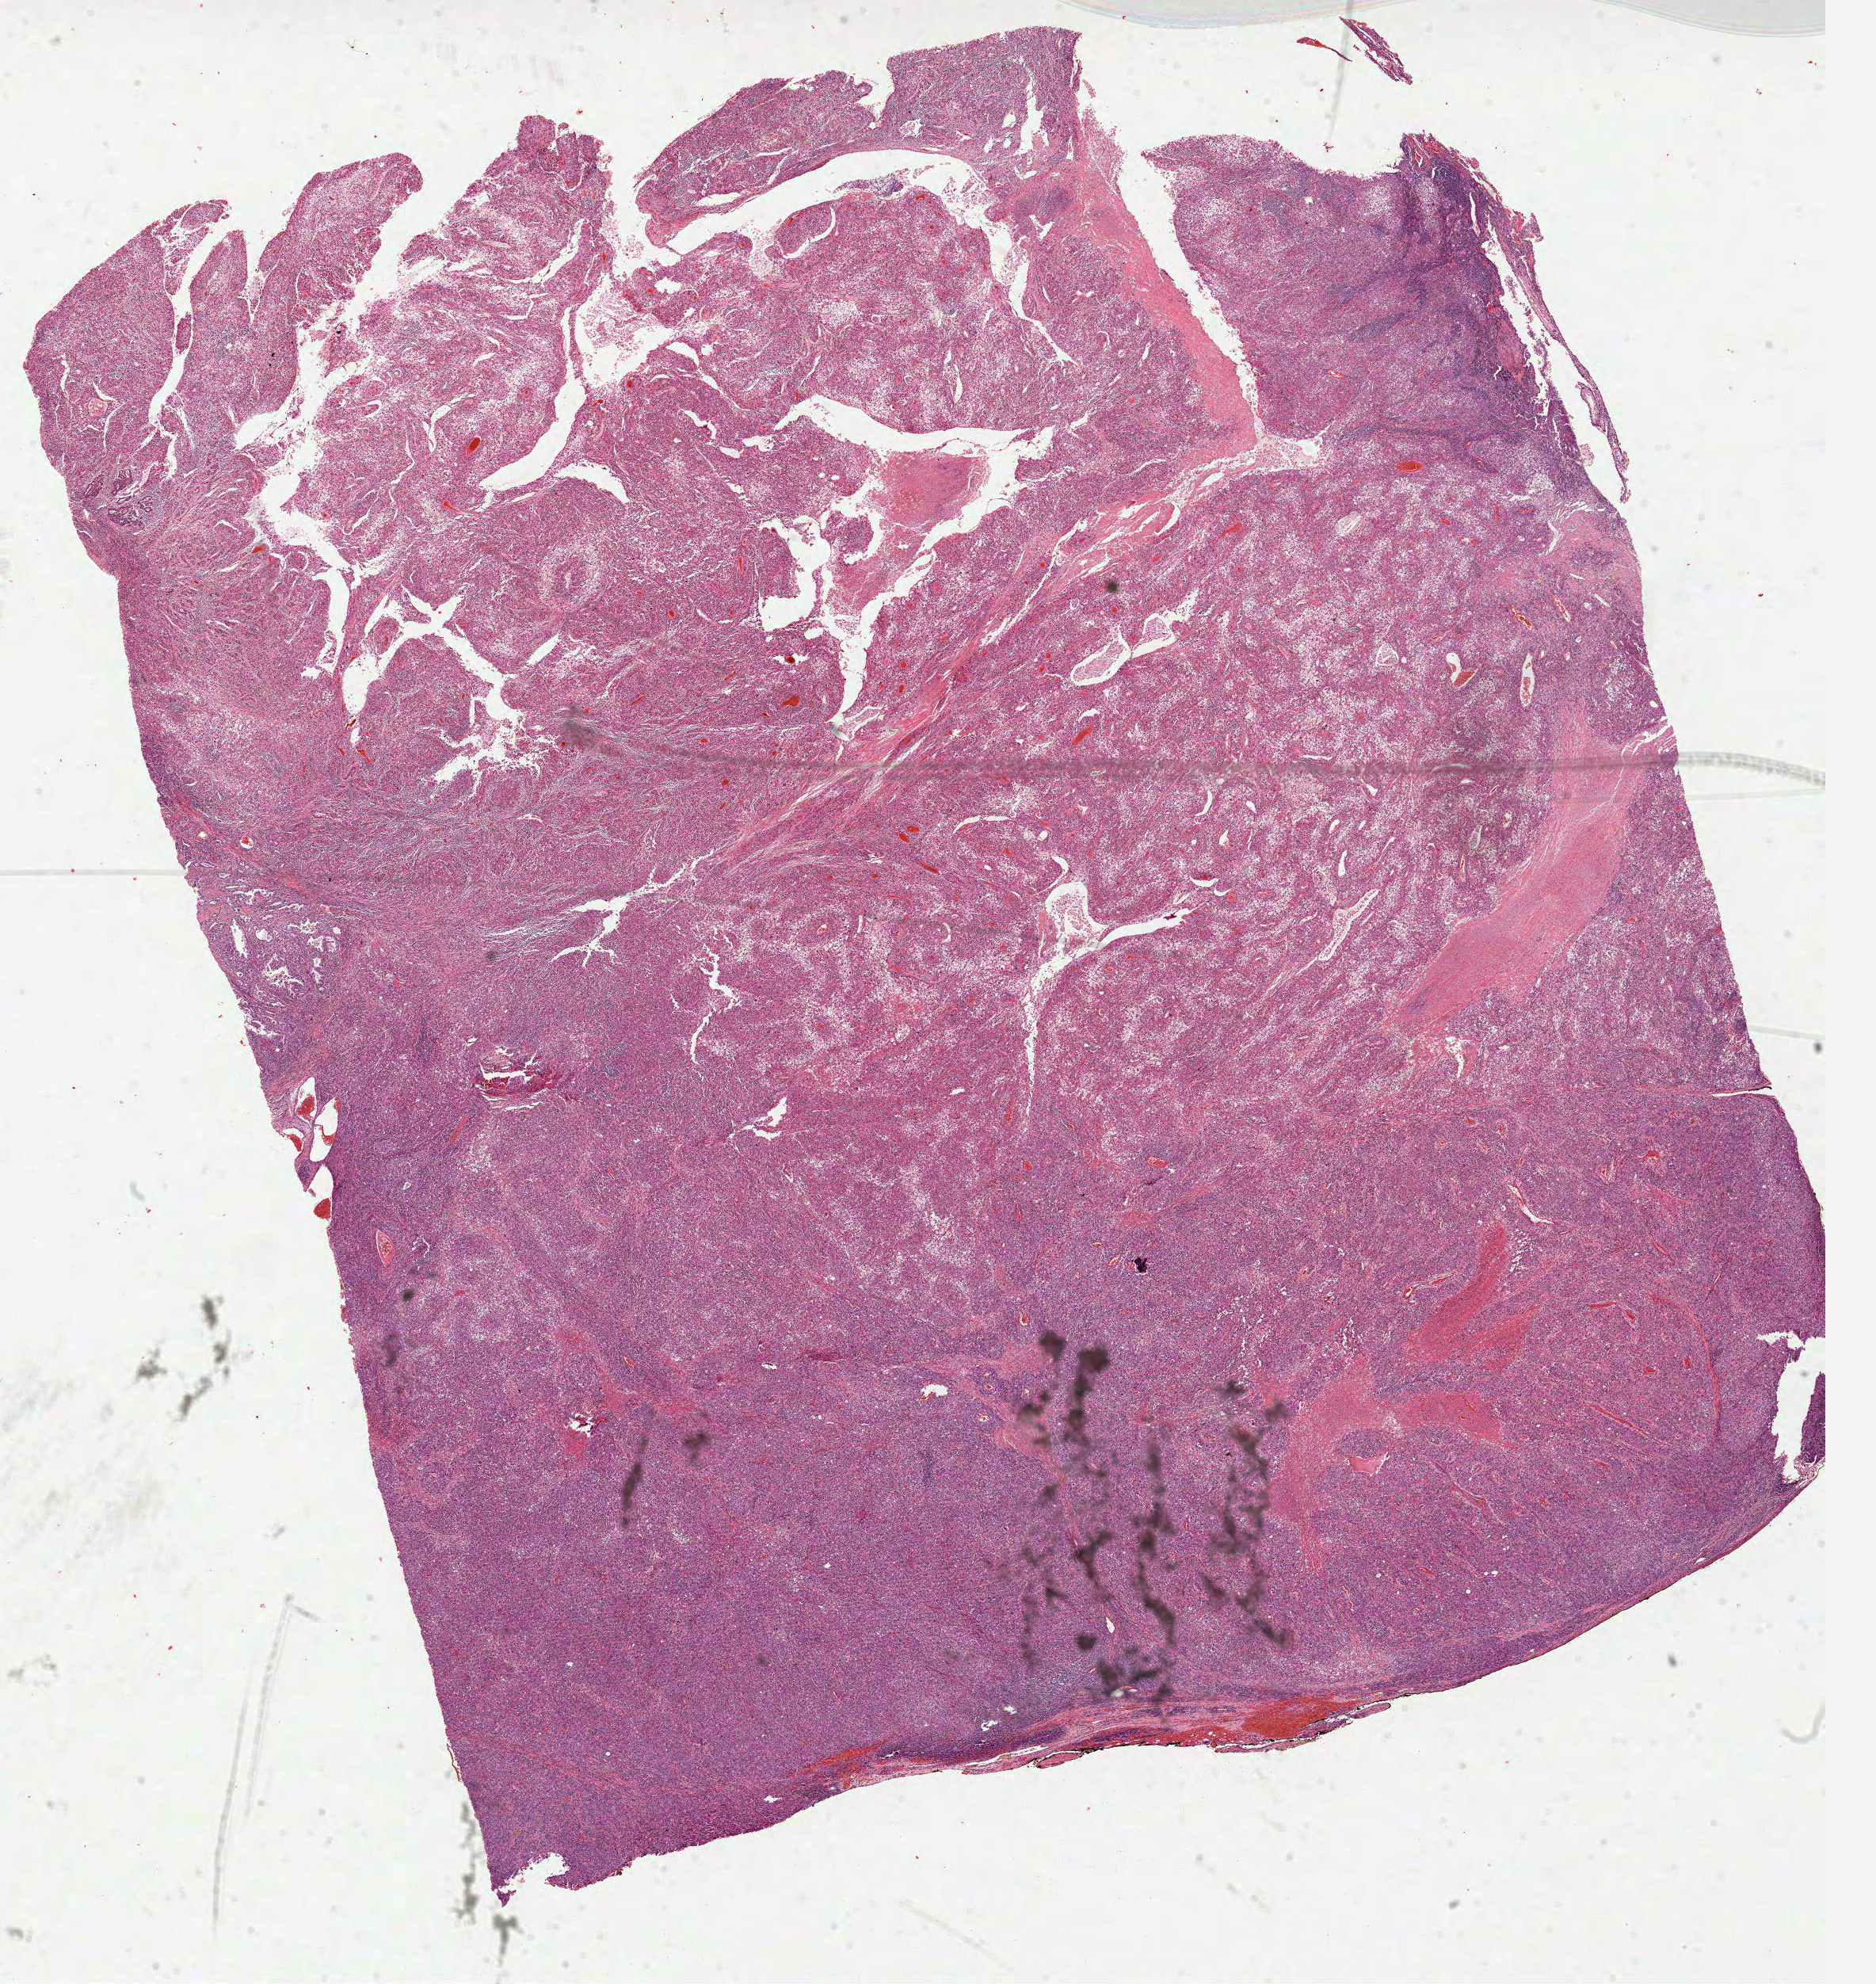
Digitized H&E tissue section (whole slide) — a low-resolution overview of the entire scanned area, about 19.1 x 20.2 mm (acquisition: 40x scan), formalin-fixed paraffin-embedded (FFPE) diagnostic section, primary tumour sample from the lung. Patient: female, age at initial diagnosis 40 years.
AJCC pathologic stage: IV. Diagnosis: Adenocarcinoma, NOS (upper lobe, lung). Laterality: right.